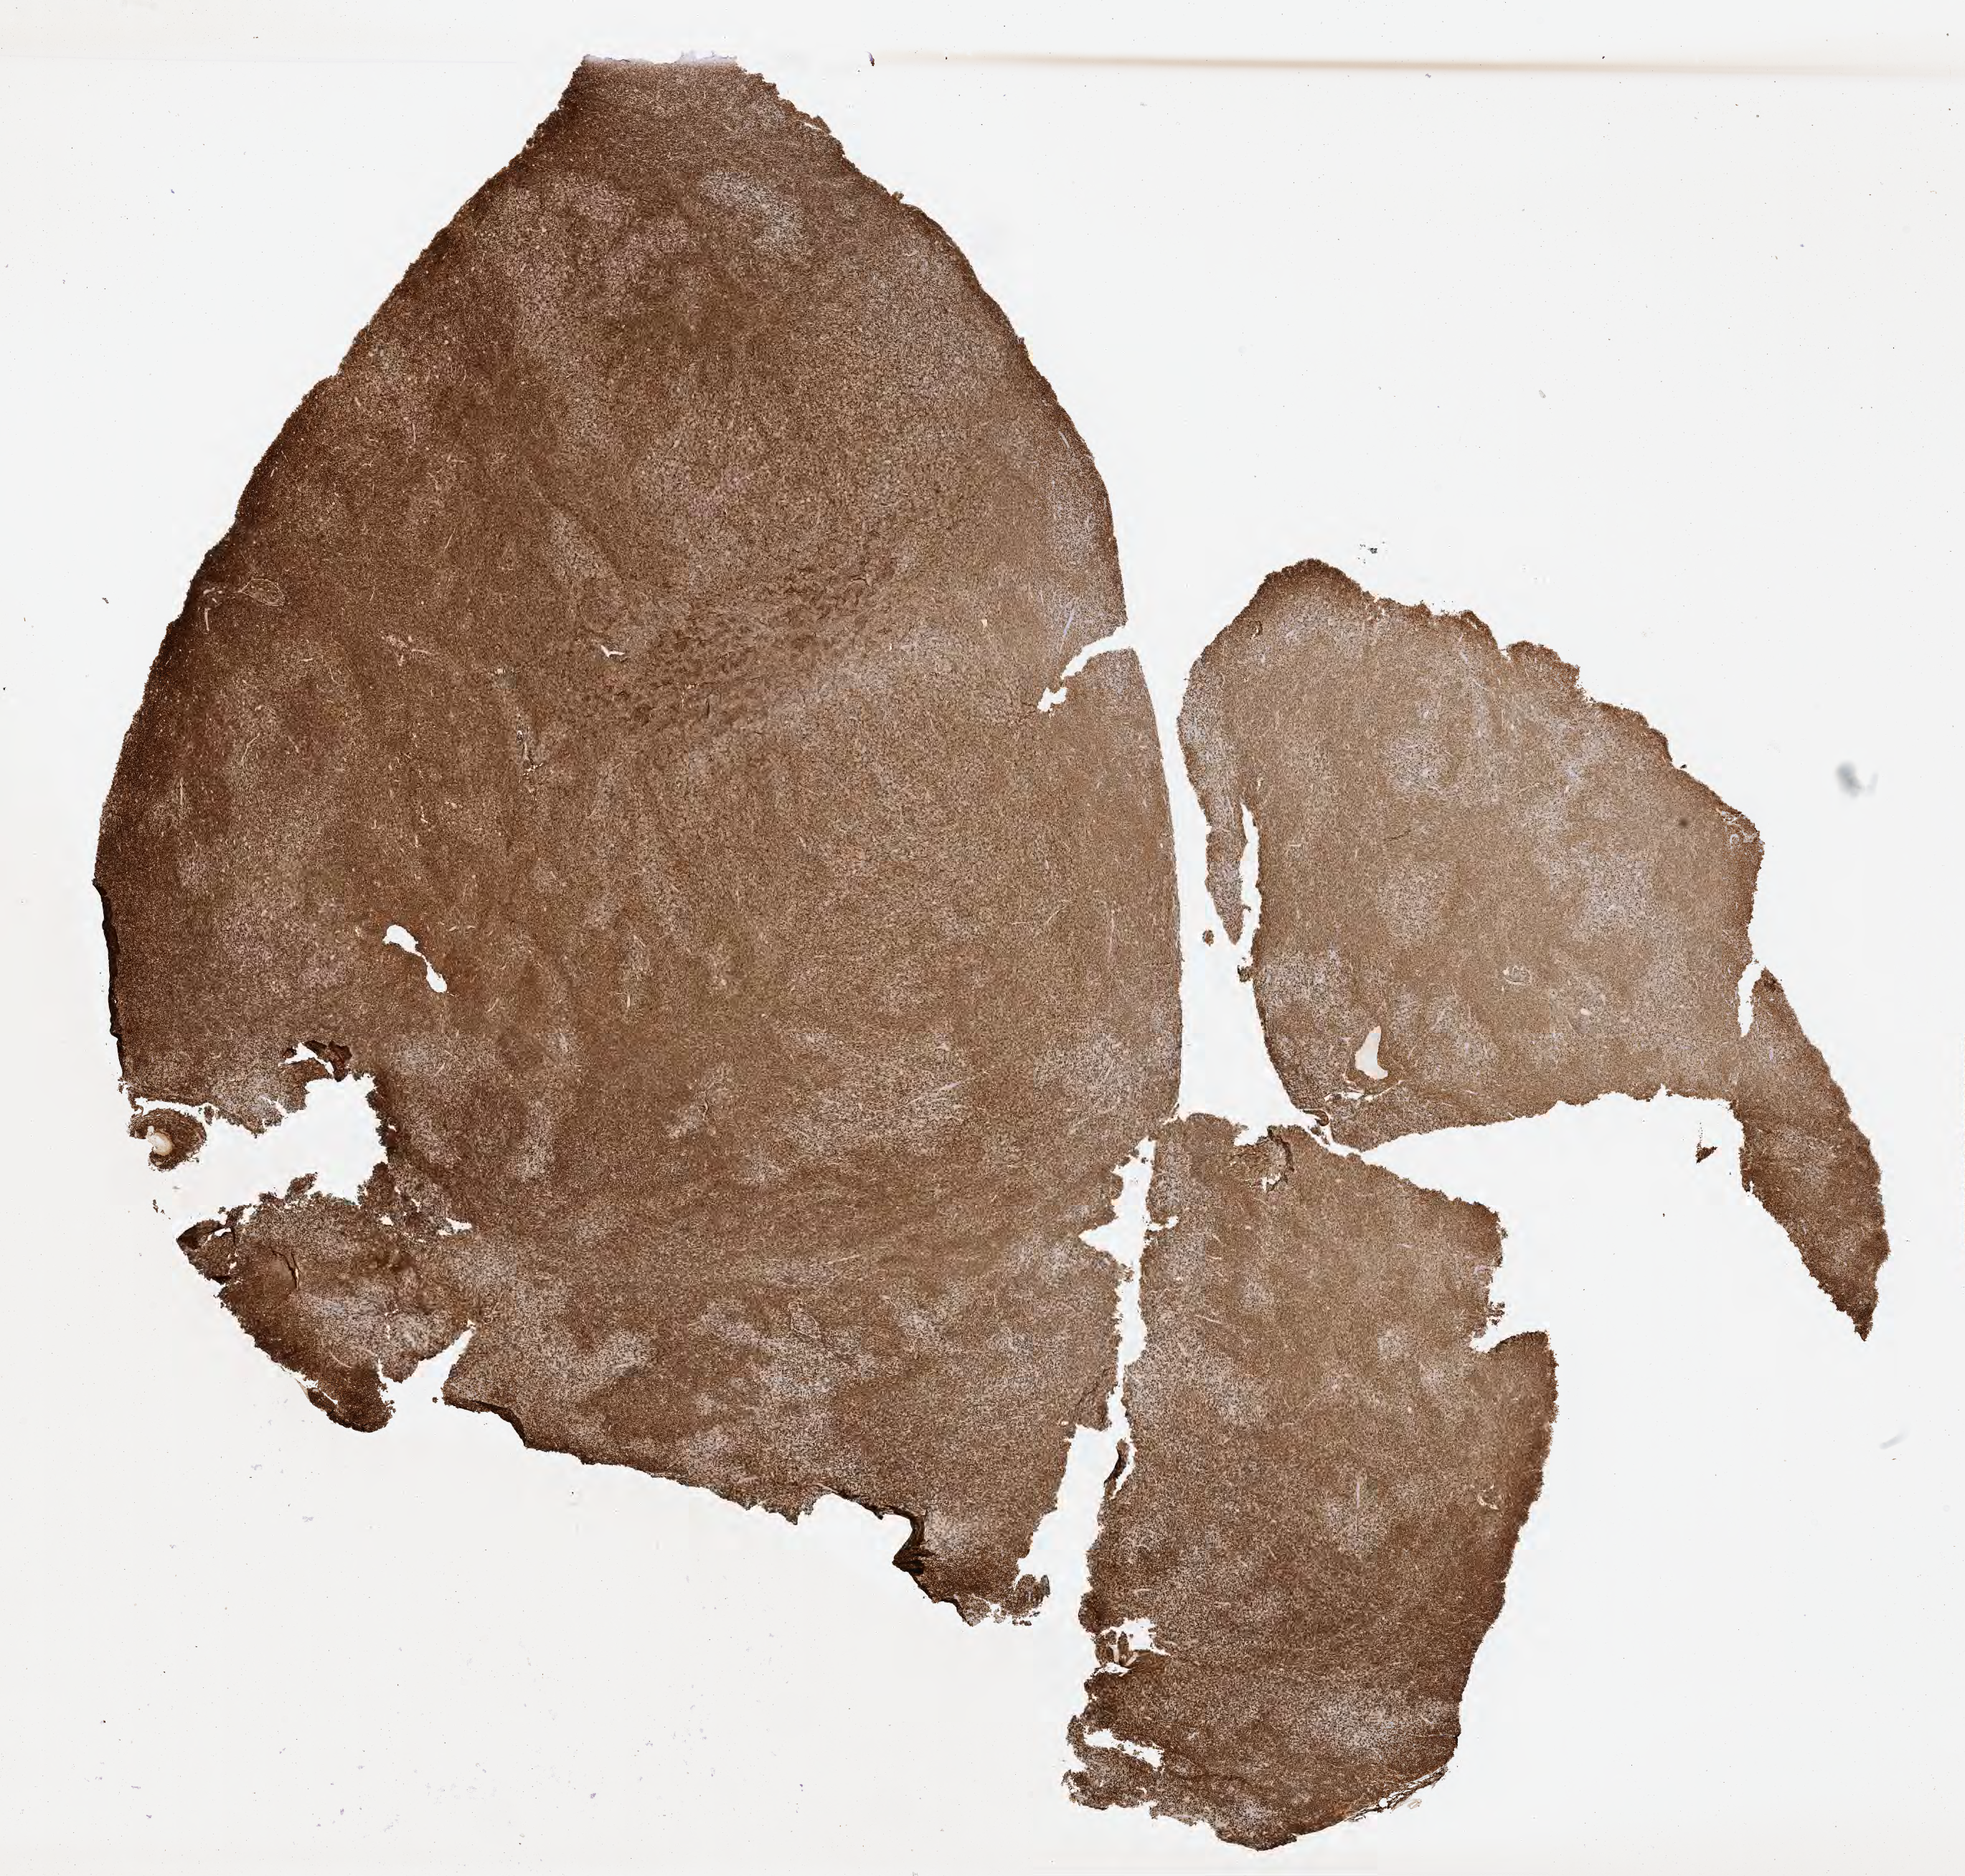
Immunohistochemistry (IHC) whole-slide image stained for CD20, low-resolution overview of the scanned area, about 22.1 x 21.1 mm. Tumor tissue. Site: liver. Patient female; aged 46.
Diagnosis: Diffuse large B-cell lymphoma, NOS.